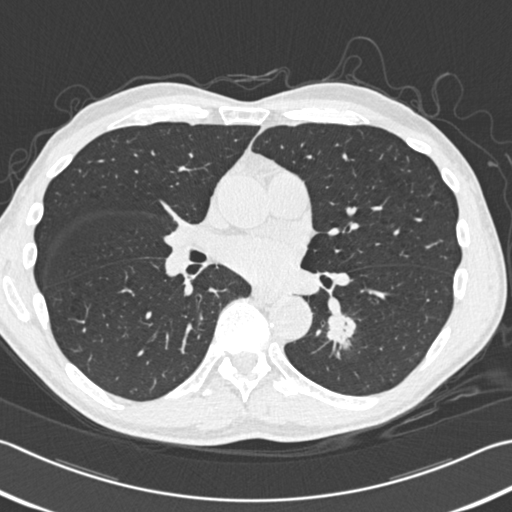
Low-dose screening chest CT, one axial slice; position 181 of 354 along the scan axis; 120 kVp; lung window (W 1500 / L -600 HU); 1 mm slice thickness; 512 × 512 image matrix.
Annotated regions visible in this slice (outlined manually by an expert reader):
- lesion 1 (tumor, lower lobe of left lung): box from (x=327, y=314) to (x=356, y=340) px